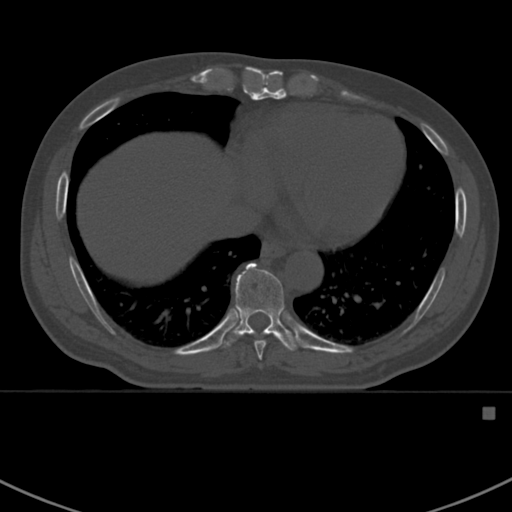
CT including the spine, one axial slice; slice 389 of 412 in the series (ordered by position); reconstruction kernel Br40s; 120 kVp; bone window (W 1800 / L 400 HU); 1.5 mm slice thickness; 512 × 512 image matrix, field of view 358 × 358 mm. Patient: male, 59 years. From the clinical record (not read from this slice): primary cancer: prostate.
Annotated regions visible in this slice (semi-automatic segmentation, software-assisted and operator-edited):
- T8 vertebra: bounding box [x1, y1, x2, y2] px = [253, 341, 266, 360]
- T9 vertebra: [218, 262, 303, 352]